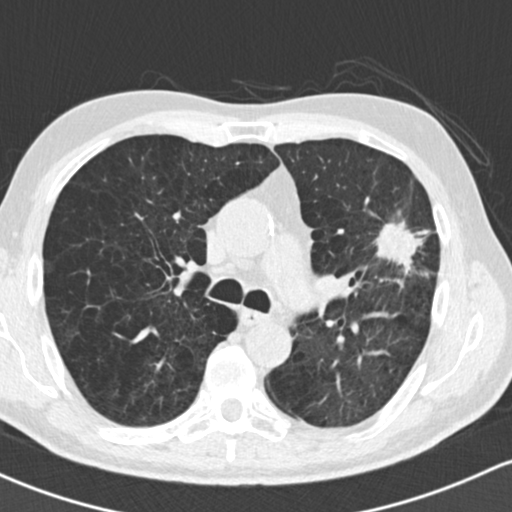
Low-dose screening chest CT, axial slice. First (baseline) screen. Lung window (W 1500 / L -600 HU). Male participant, aged 61 years at enrolment. Former smoker at enrolment.
Expert-annotated lung lesion, bounding box (x1, y1, x2, y2) in pixels: (356, 187, 456, 295). Reader record for this screening exam (exam-level; its link to the box is not recorded): non-calcified nodule or mass ≥4 mm, left upper lobe, 35 × 35 mm, spiculated (stellate) margins, soft tissue attenuation. Official screen result: positive, change unspecified: nodule(s) >= 4 mm or enlarging nodule(s), mass(es), or other non-specific abnormalities suspicious for lung cancer. Later outcome: lung cancer diagnosed 19 days after this screen — adenocarcinoma, NOS, left upper lobe, well differentiated (G1), stage IIIA (AJCC 6th edition), 45 mm at pathology.